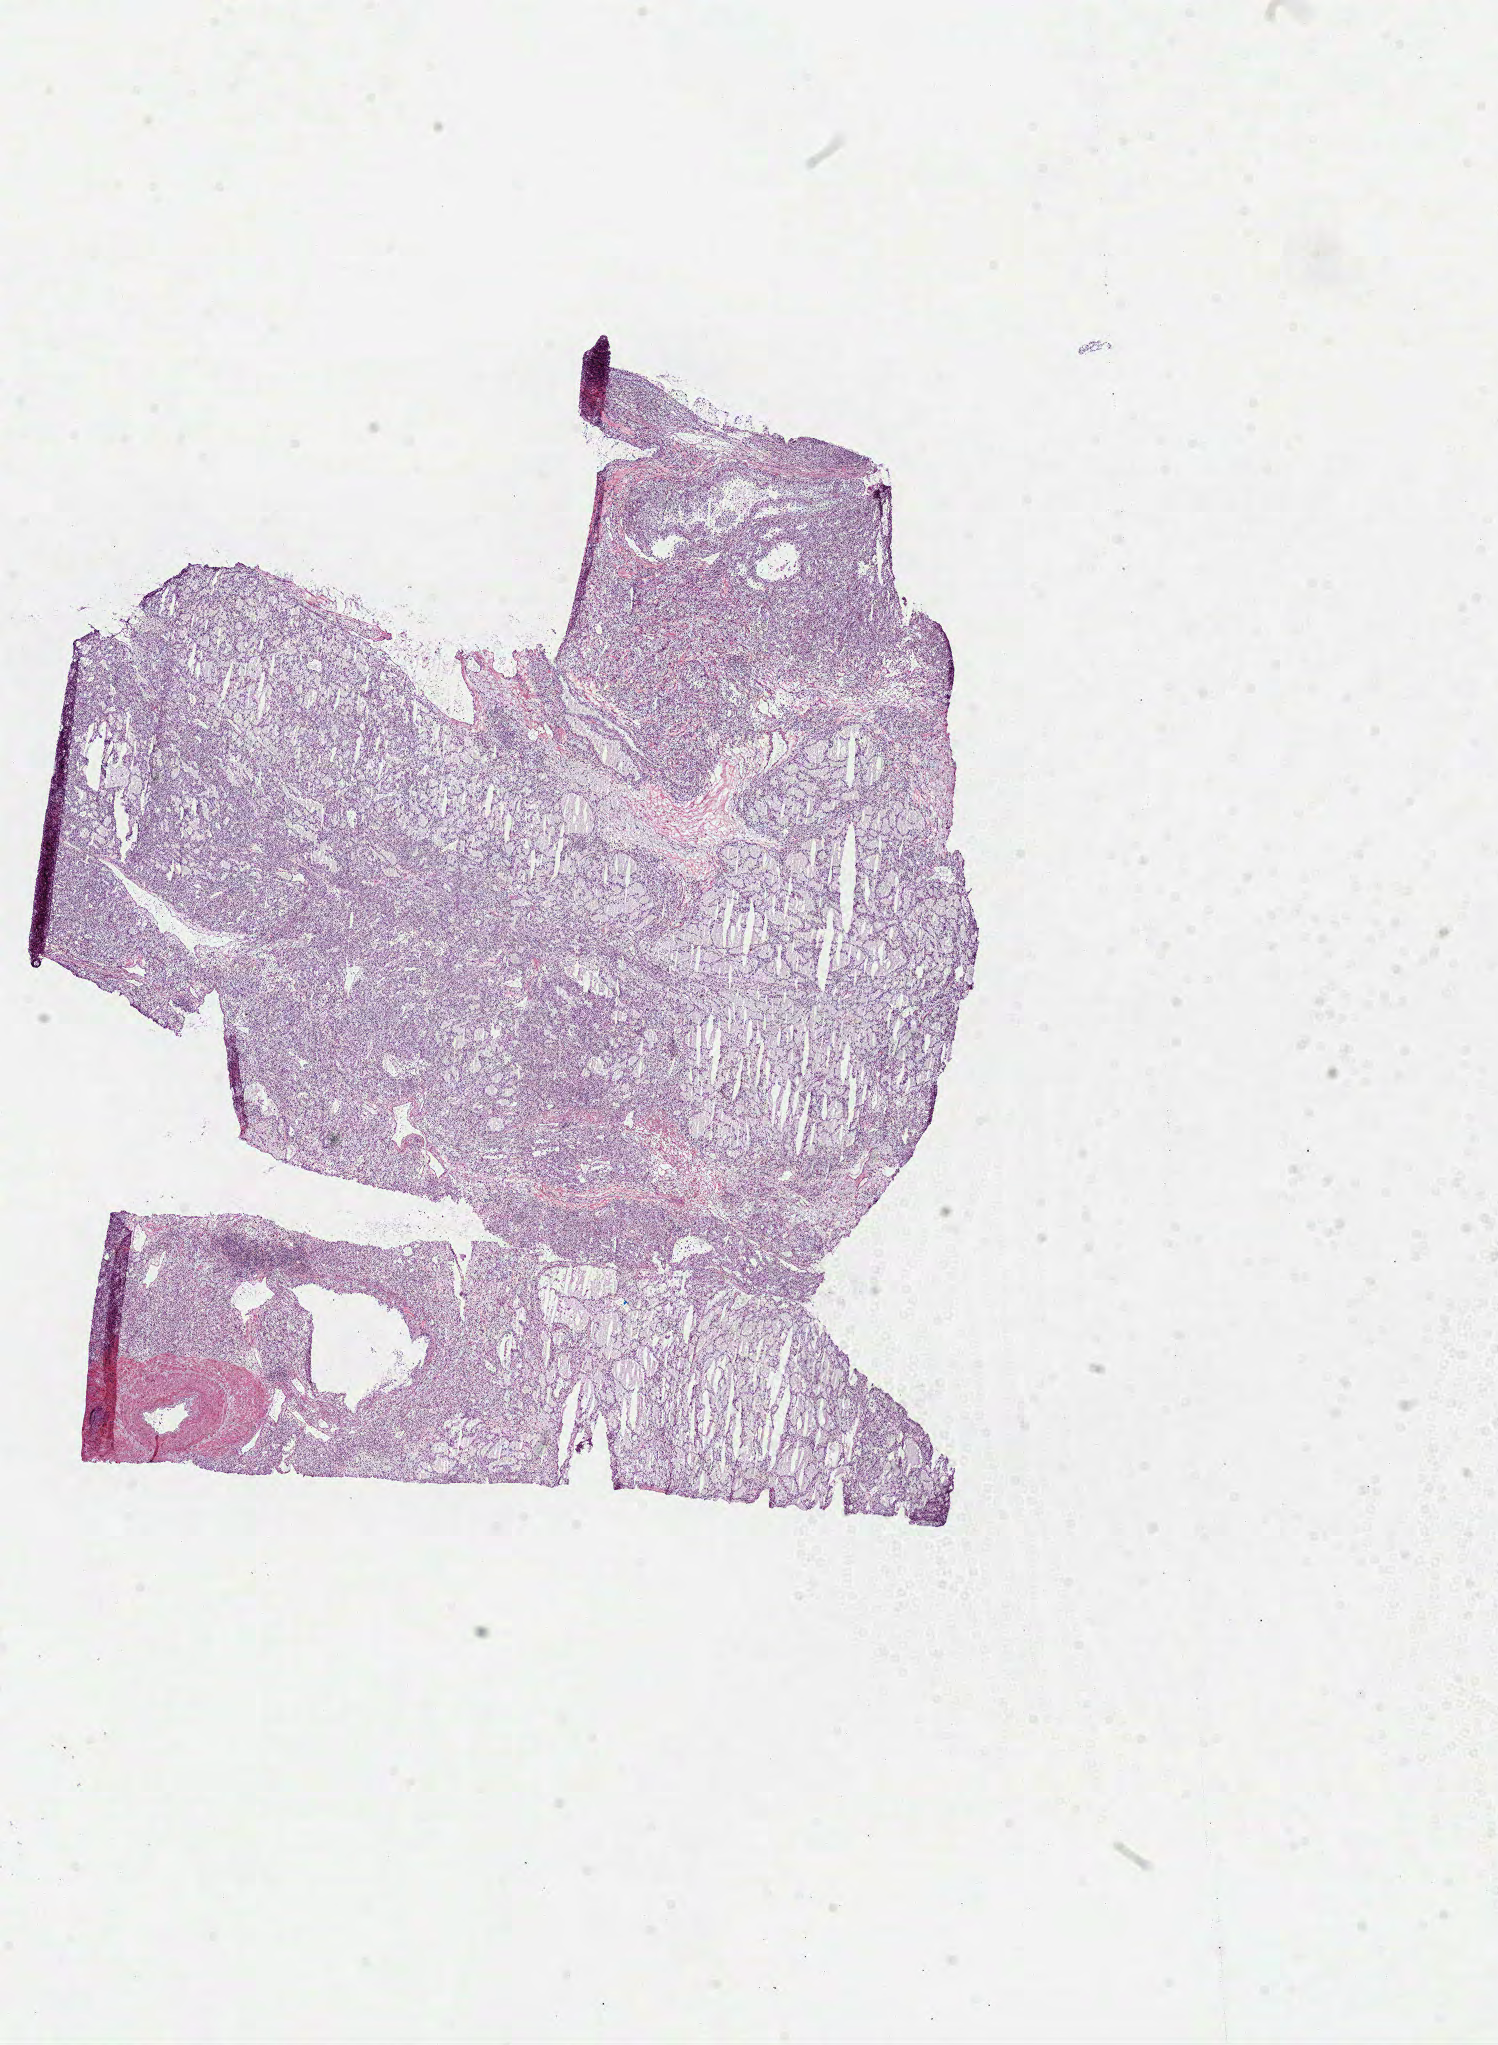
H&E whole-slide image, low-resolution overview of the scanned area, about 12.1 x 16.5 mm (acquisition: 40x scan), frozen section, kidney, primary tumour sample. Female patient; age at initial diagnosis 67 years. Composition of this section per pathologist review: tumour cells 90%, tumour nuclei 85%.
Pathologic diagnosis: Clear cell adenocarcinoma, NOS.